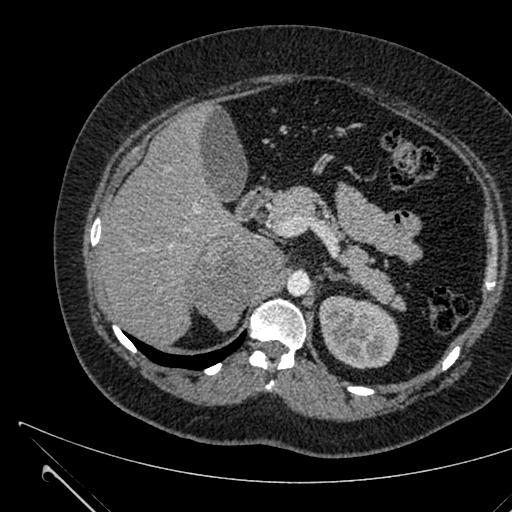
Contrast-enhanced abdominal CT, one axial slice. Position 426 of 731 along the scan axis. 120 kVp. Intravenous contrast given. Soft-tissue window (W 400 / L 40 HU). 1 mm slice thickness. 512 × 512 image matrix. Female patient, age 36 years. From the clinical record (not read from this slice): diagnosis: adrenocortical carcinoma; tumour side: right adrenal; tumour size at pathology: 10 cm; Ki-67 index: 20 %; stage (as recorded): 4.
Structures marked on this image (semi-automatic segmentation, software-assisted and operator-edited):
- mass: box from (x=196, y=240) to (x=282, y=330) px